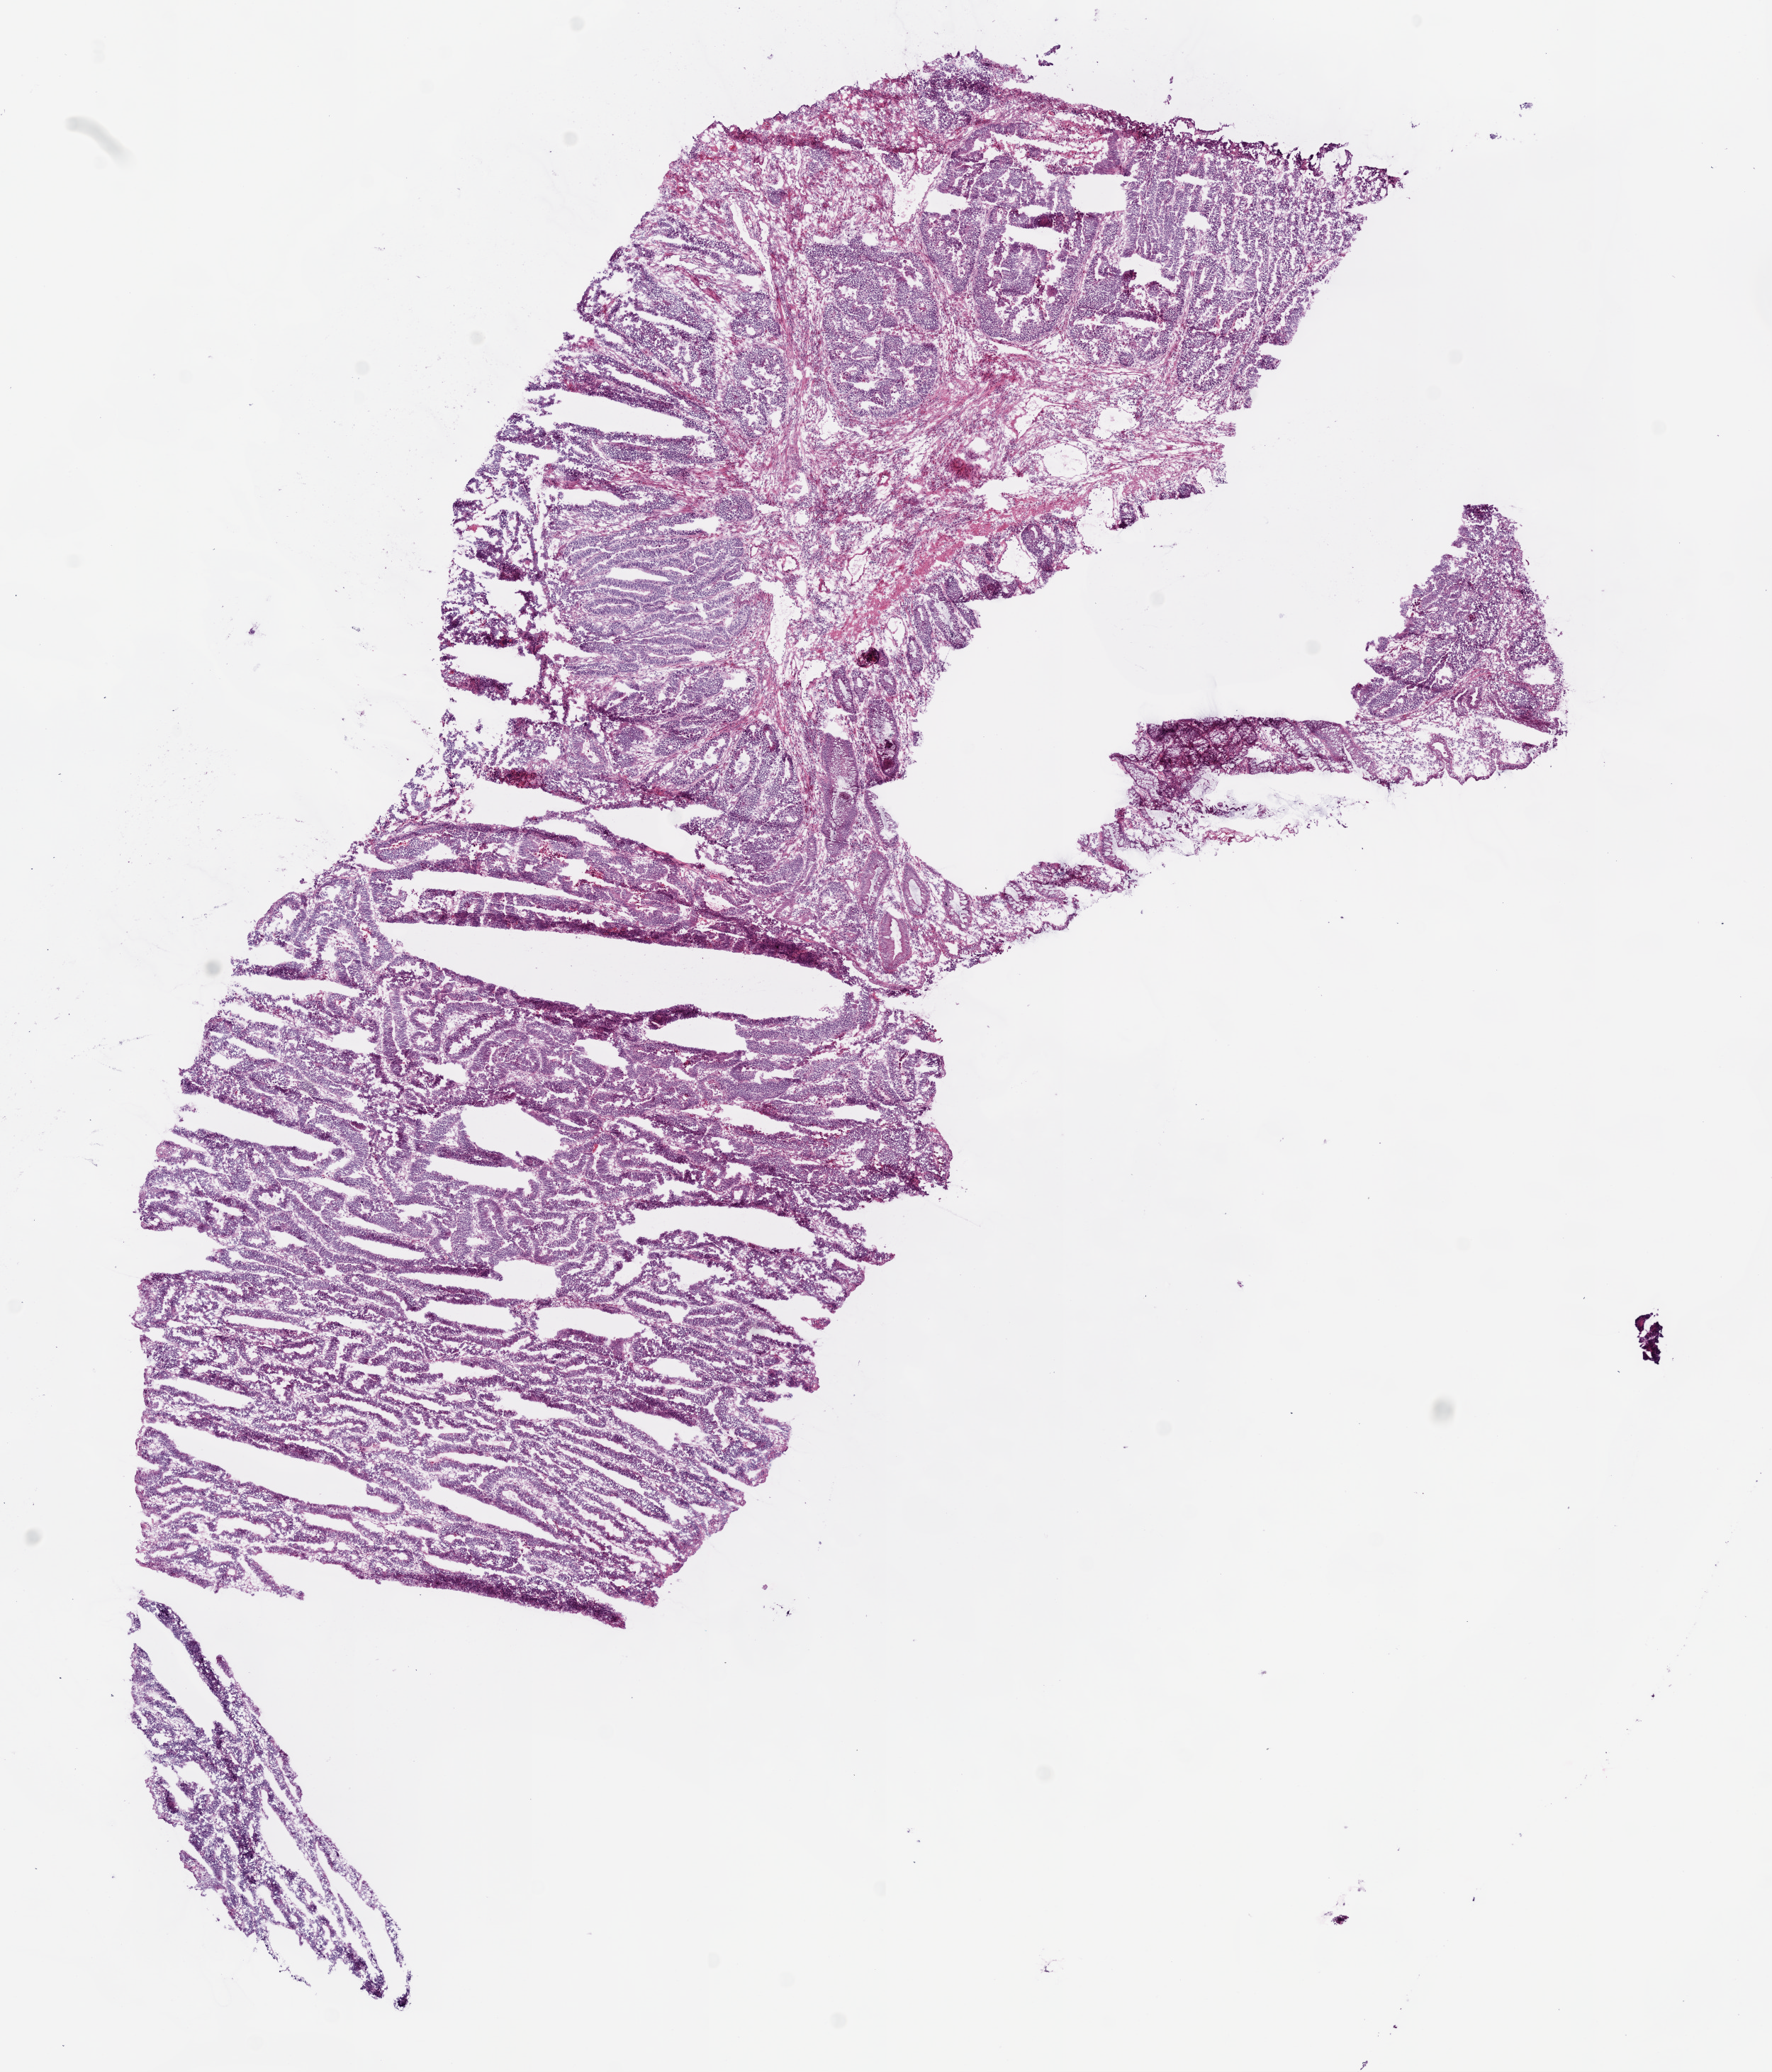
Digitized H&E tissue section (whole slide), low-resolution overview of the scanned area, about 10.0 x 11.7 mm (from a 20x scan), frozen section from the bottom of the tissue portion, sample: primary tumour, colon. Patient: male, age at initial diagnosis 63 years. Composition of this section per pathologist review: tumour cells 95%, tumour nuclei 95%, normal cells 0%, stromal cells 5%, necrosis 0%.
- AJCC pathologic stage: III (5th edition)
- lymph nodes positive (case pathology): 3 of 43 examined
- TNM: T3 N1 M0
- pathologic diagnosis: Adenocarcinoma, NOS